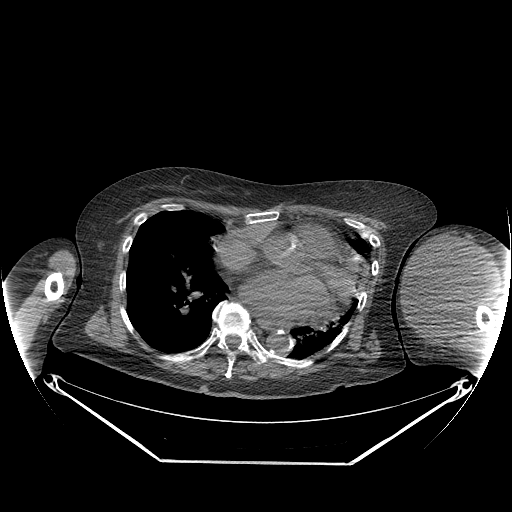
CT of an extremity soft-tissue mass (from a PET/CT study), one axial slice. Position 163 of 267 along the scan axis. 140 kVp. Soft-tissue window (W 400 / L 40 HU). 3.75 mm slice thickness. 512 × 512 image matrix. Female patient. Case-level facts recorded for this patient, not image findings: histological type: pleiomorphic leiomyosarcoma; grade: high; site of the primary tumour: left biceps.
Annotated regions visible in this slice (expert contour drawn on MRI and transferred to this co-registered scan by the dataset authors):
- gross tumour volume including surrounding oedema: box from (x=402, y=235) to (x=490, y=330) px
- gross tumour volume (mass): (x=402, y=235)–(x=490, y=328)